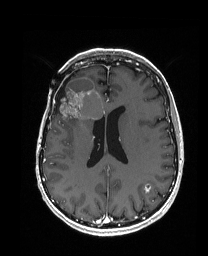
Brain MRI from a brain-tumour surgery series, one axial slice; slice 77 of 192 in the series (ordered by position); T1-weighted post-contrast; 1 mm slice thickness; 208 × 256 image matrix, field of view 203 × 250 mm. From the clinical record (not read from this slice): histopathology: Metastatic Carcinoma from Breast primary; tumour location: Right Frontal.
Annotated regions visible in this slice (manually delineated by an expert):
- previous resection cavity: bounding box <54,77,71,114> (left, top, right, bottom; pixels)
- tumour: <55,77,104,128>